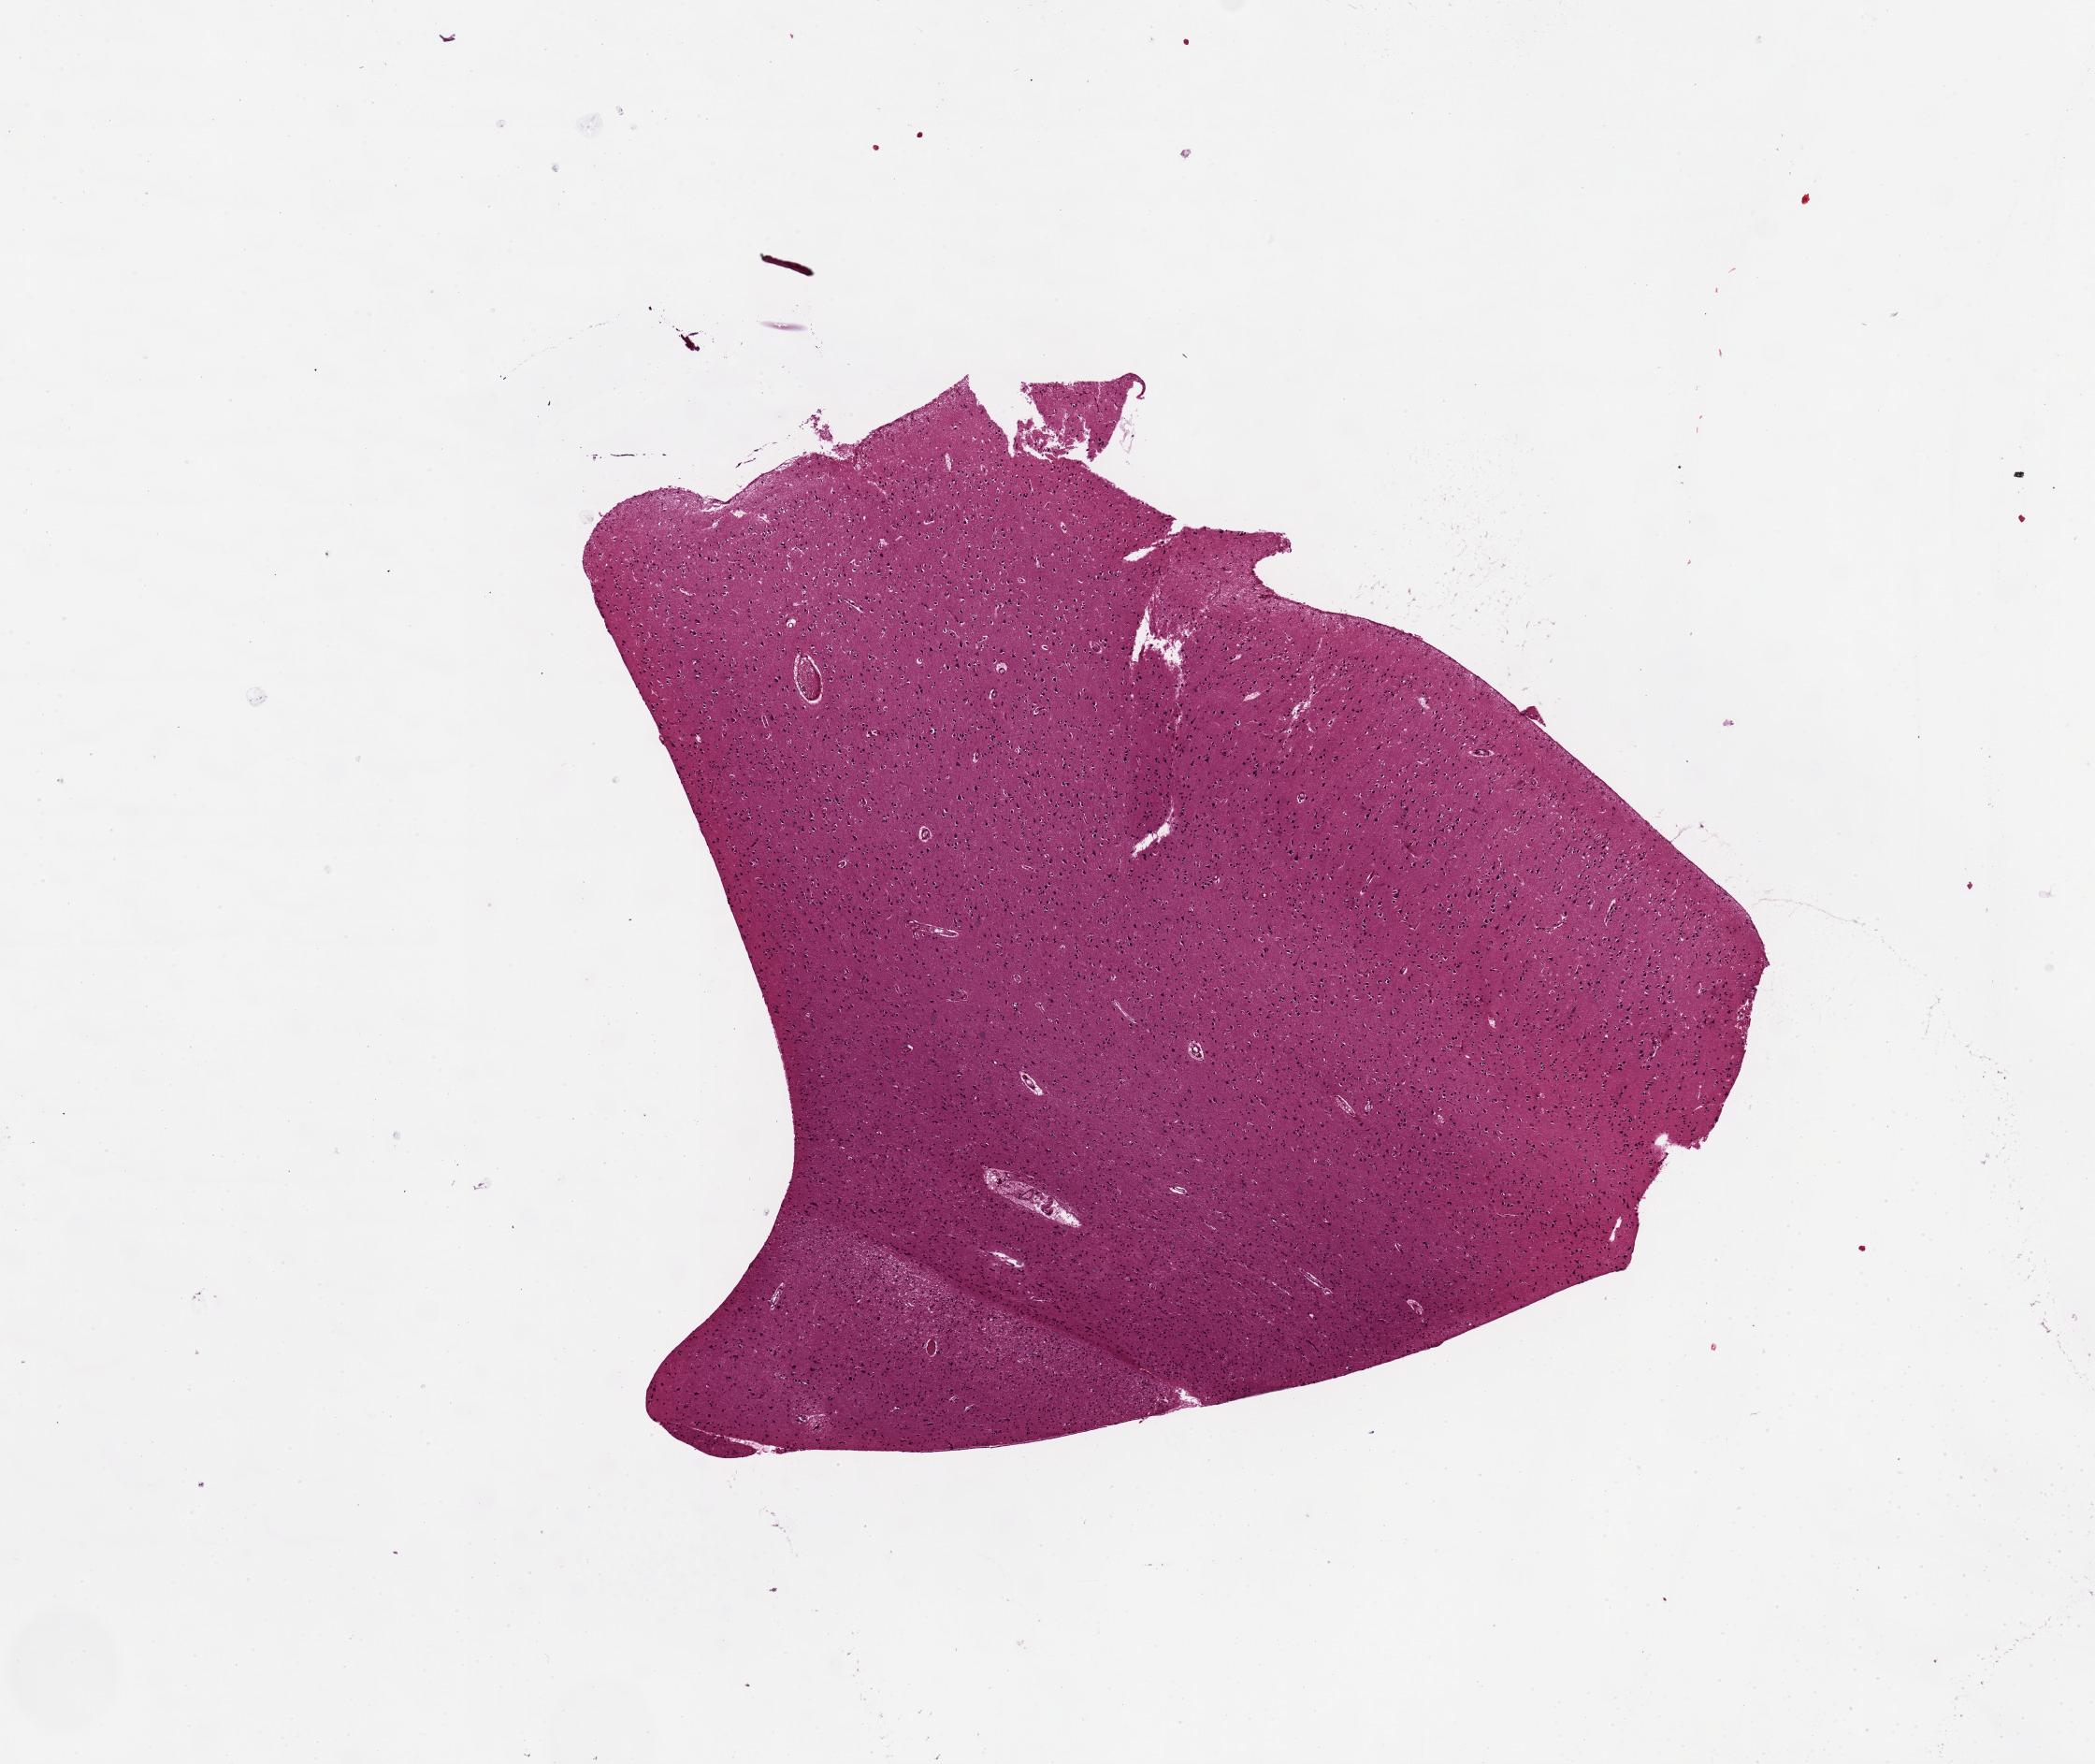
Hematoxylin and eosin (H&E) whole-slide image, brightfield, shown as a low-resolution overview of the whole scanned area (about 8.9 x 7.5 mm, slide scanned at 20x); PAXgene-fixed paraffin-embedded (PFPE) section; target tissue: cerebral cortex; tissue donor sample. Donor sex: male.
- review note (as recorded): 4.9x4.4mm